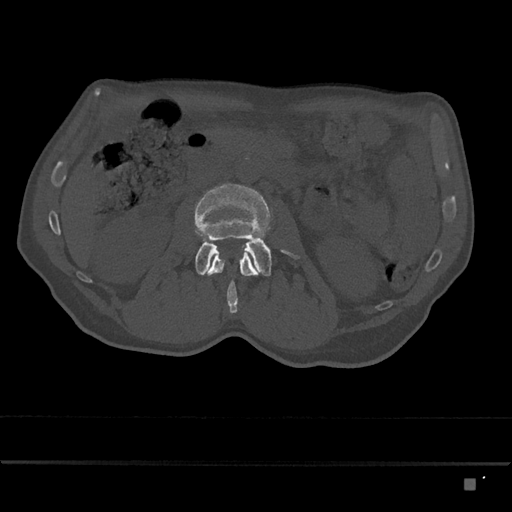
CT including the spine, one axial slice; slice 435 of 797 in the series (ordered by position); reconstruction kernel Br40s/3; 120 kVp; bone window (W 1800 / L 400 HU); 0.5 mm slice thickness; 512 × 512 image matrix, field of view 390 × 390 mm. Patient: male, 72 years. Case-level facts recorded for this patient, not image findings: primary cancer: prostate.
Annotated regions visible in this slice (semi-automatically segmented with operator editing):
- L2 vertebra: box from (x=205, y=249) to (x=258, y=314) px
- L3 vertebra: (x=194, y=184)–(x=299, y=276)